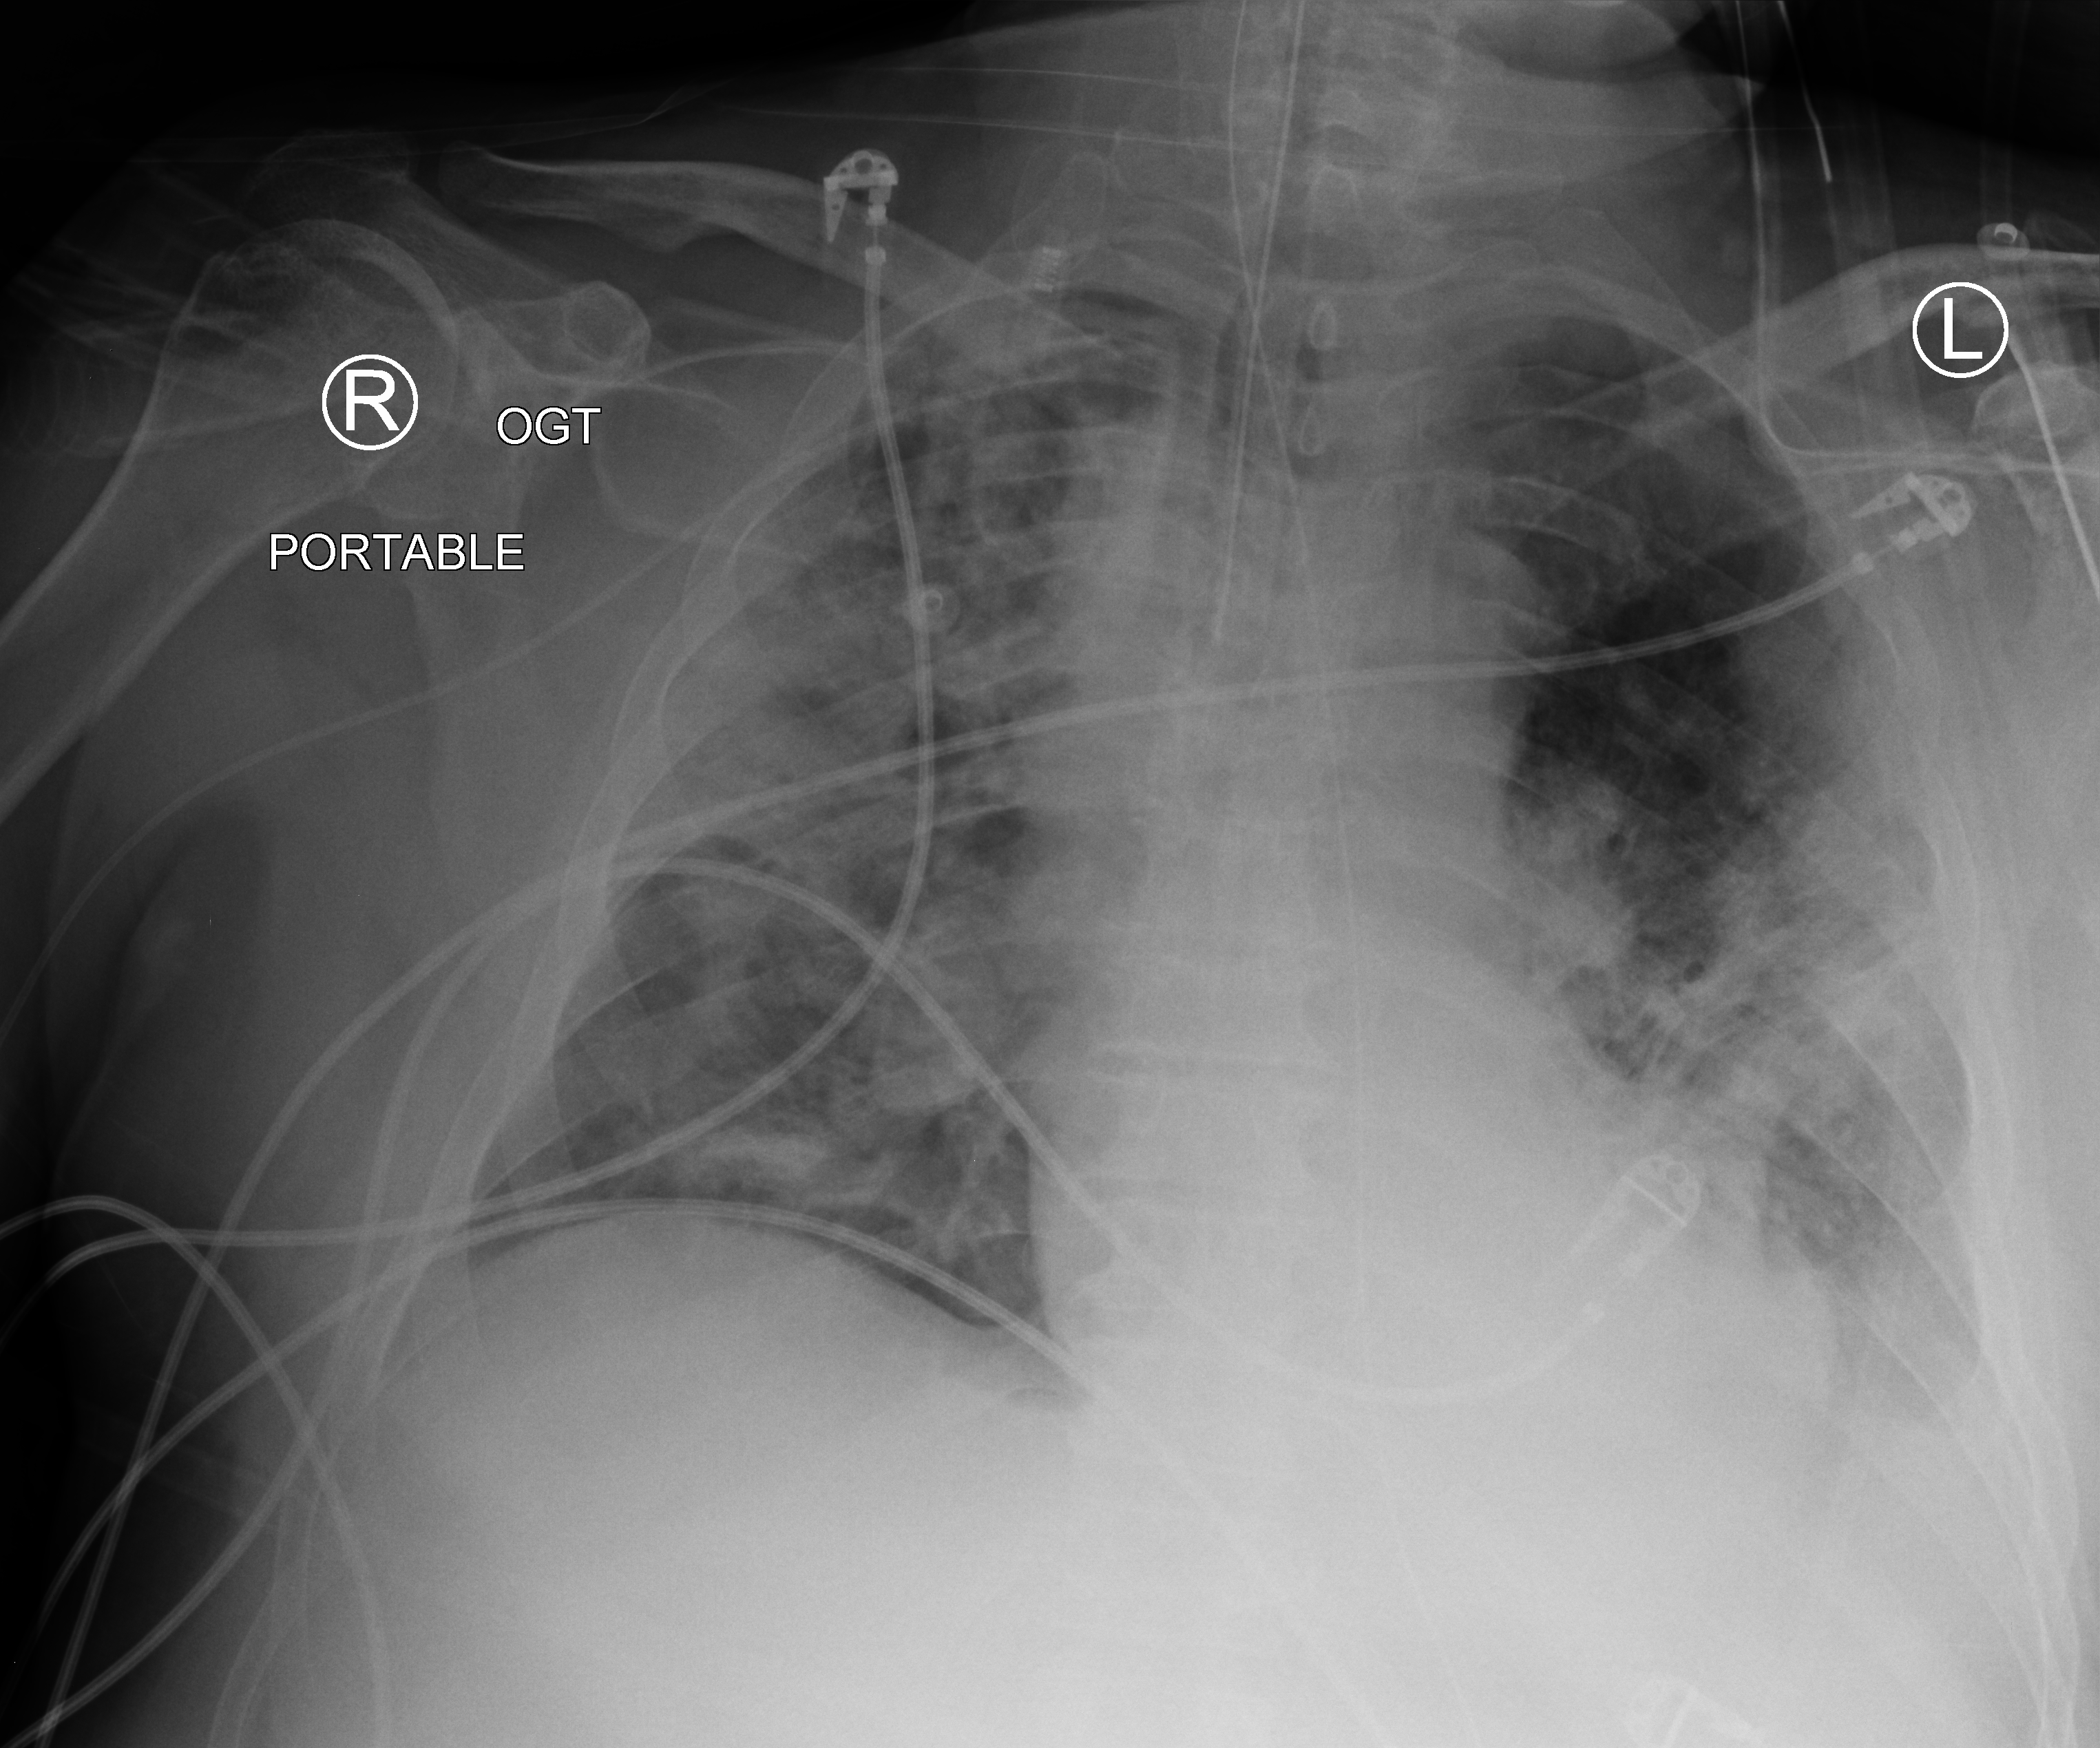
Portable chest radiograph; anteroposterior (AP) projection. Patient hospitalised with COVID-19; male, aged 60–74 years.
Admission-level facts for this patient (not findings on this image; timing relative to this image not recorded): length of hospital stay: 24 days.